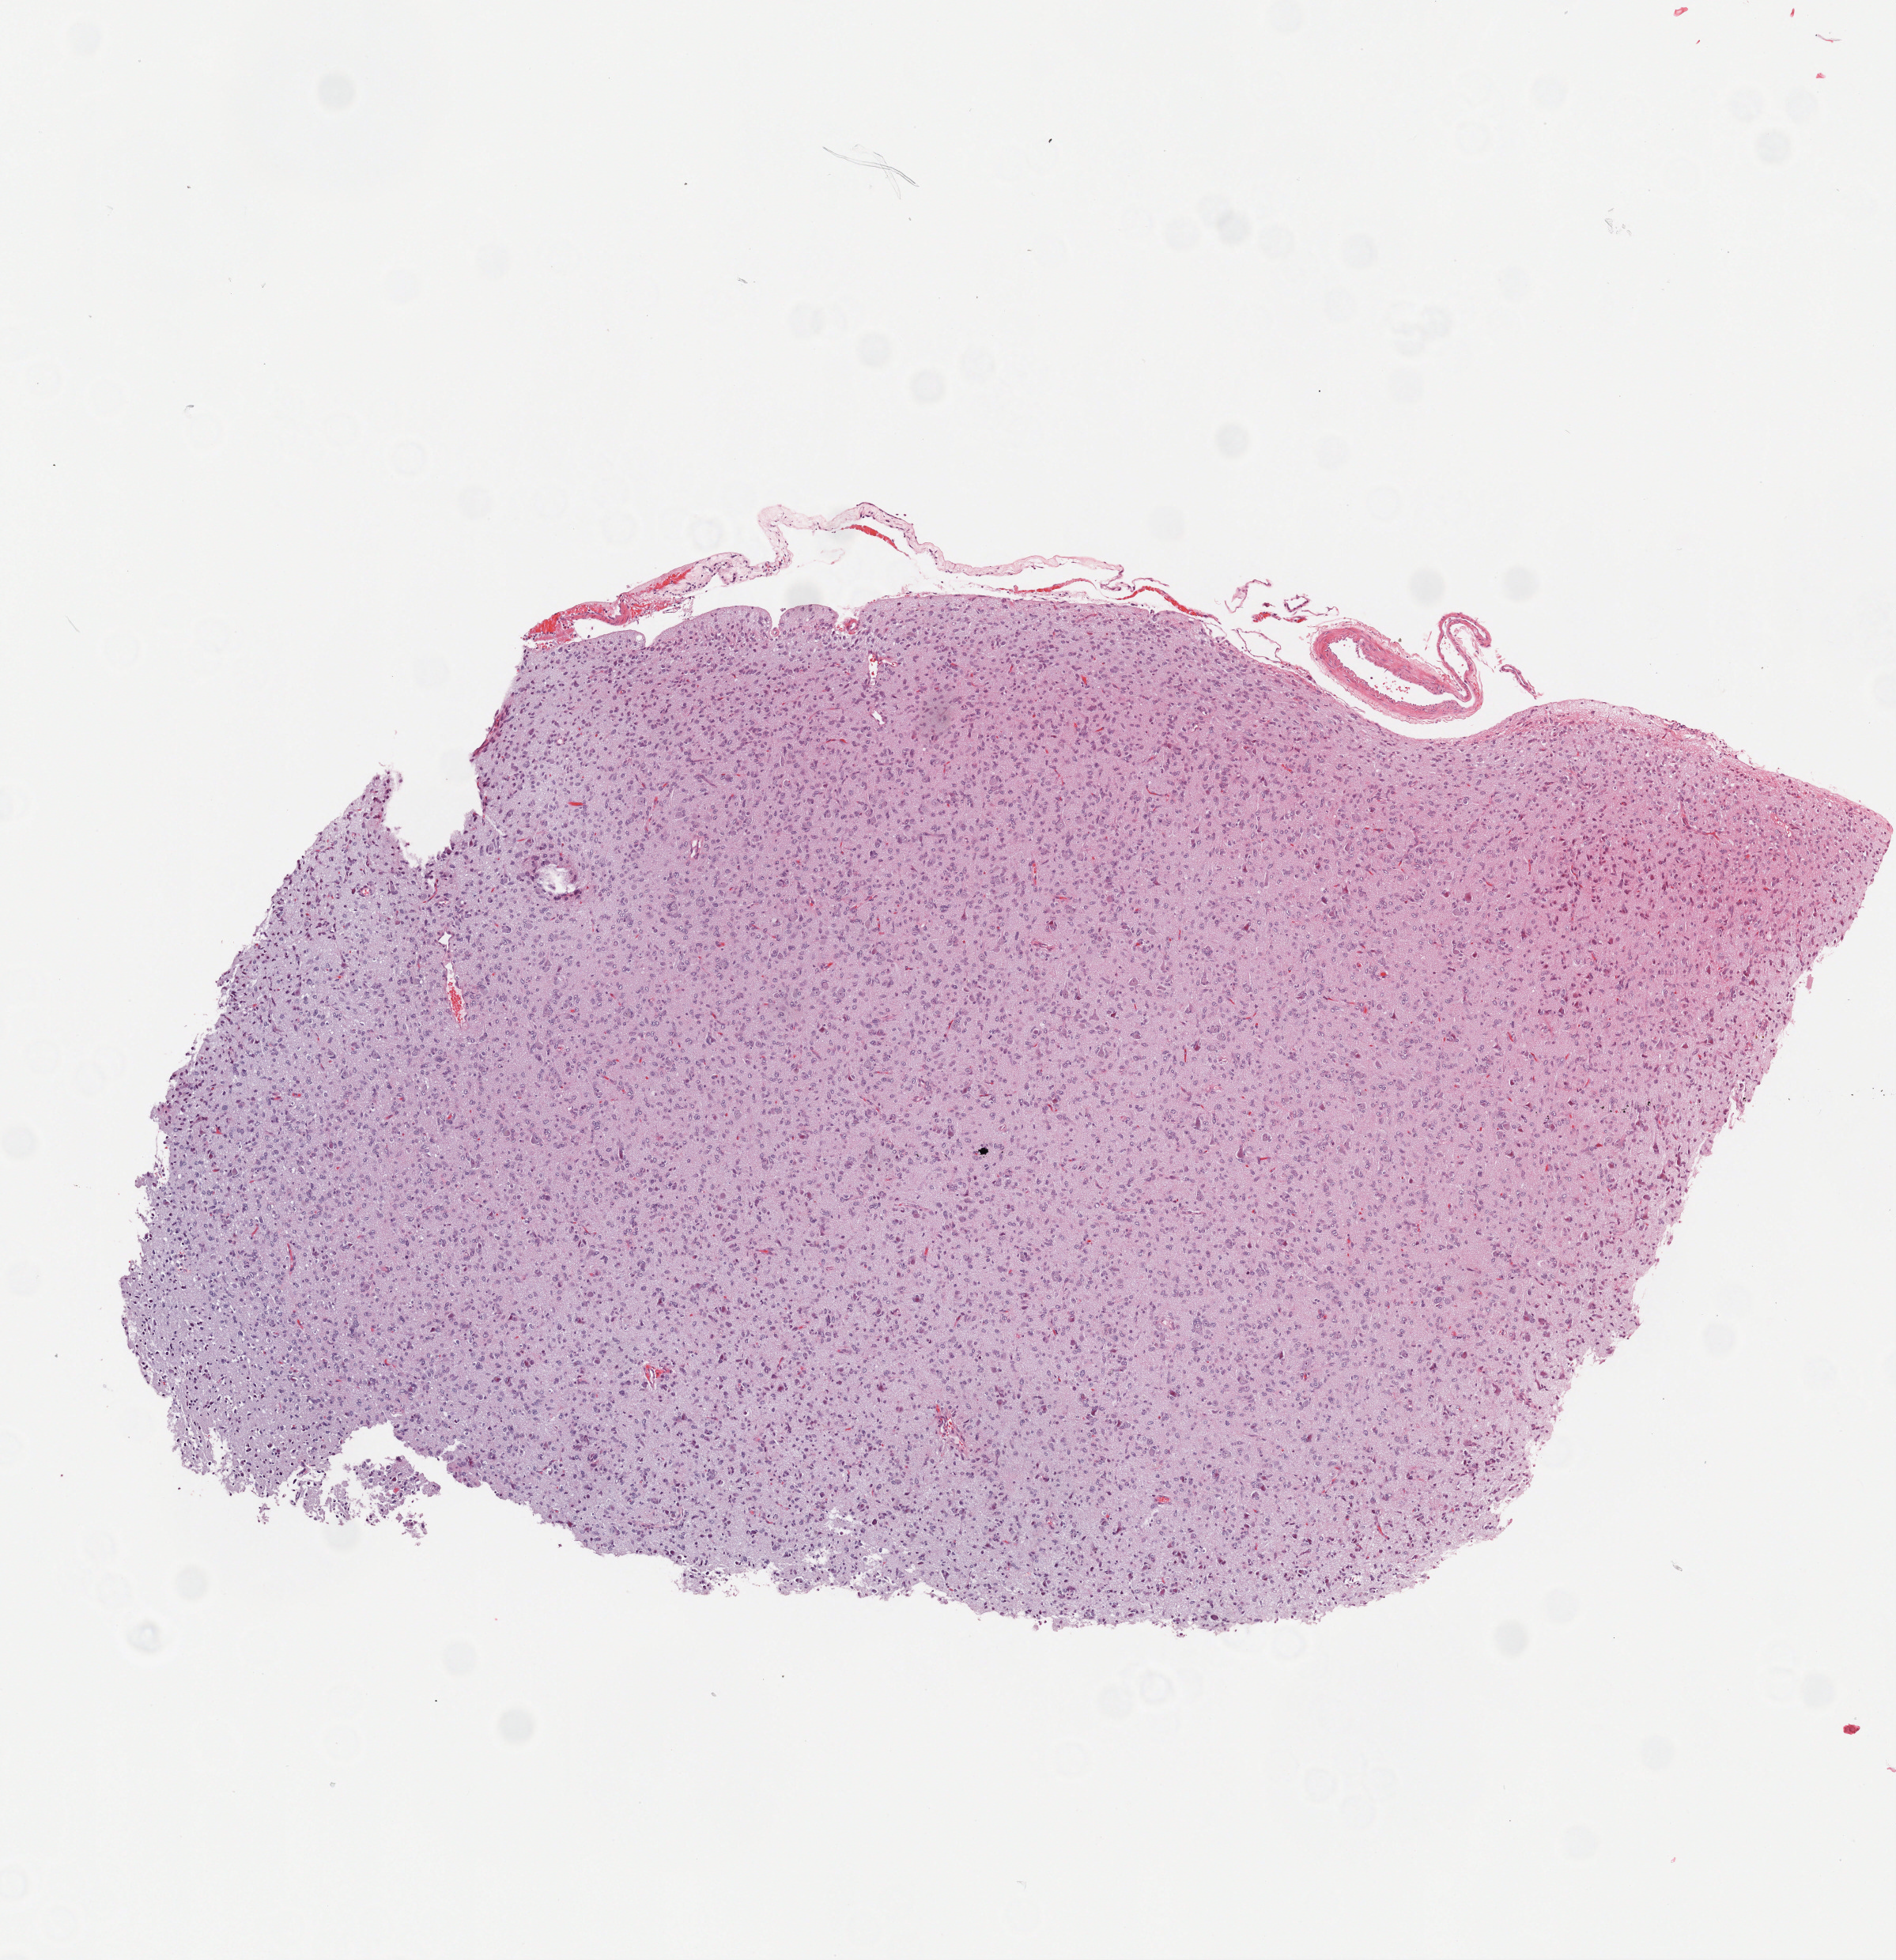
Whole-slide histology image, H&E-stained, a low-resolution overview of the entire scanned area, about 4.8 x 5.0 mm; FFPE section; primary tumour sample from the brain. Female, age 61 years at initial diagnosis. Histologic grade: G3 (poorly differentiated).
Histologic diagnosis: Mixed glioma.